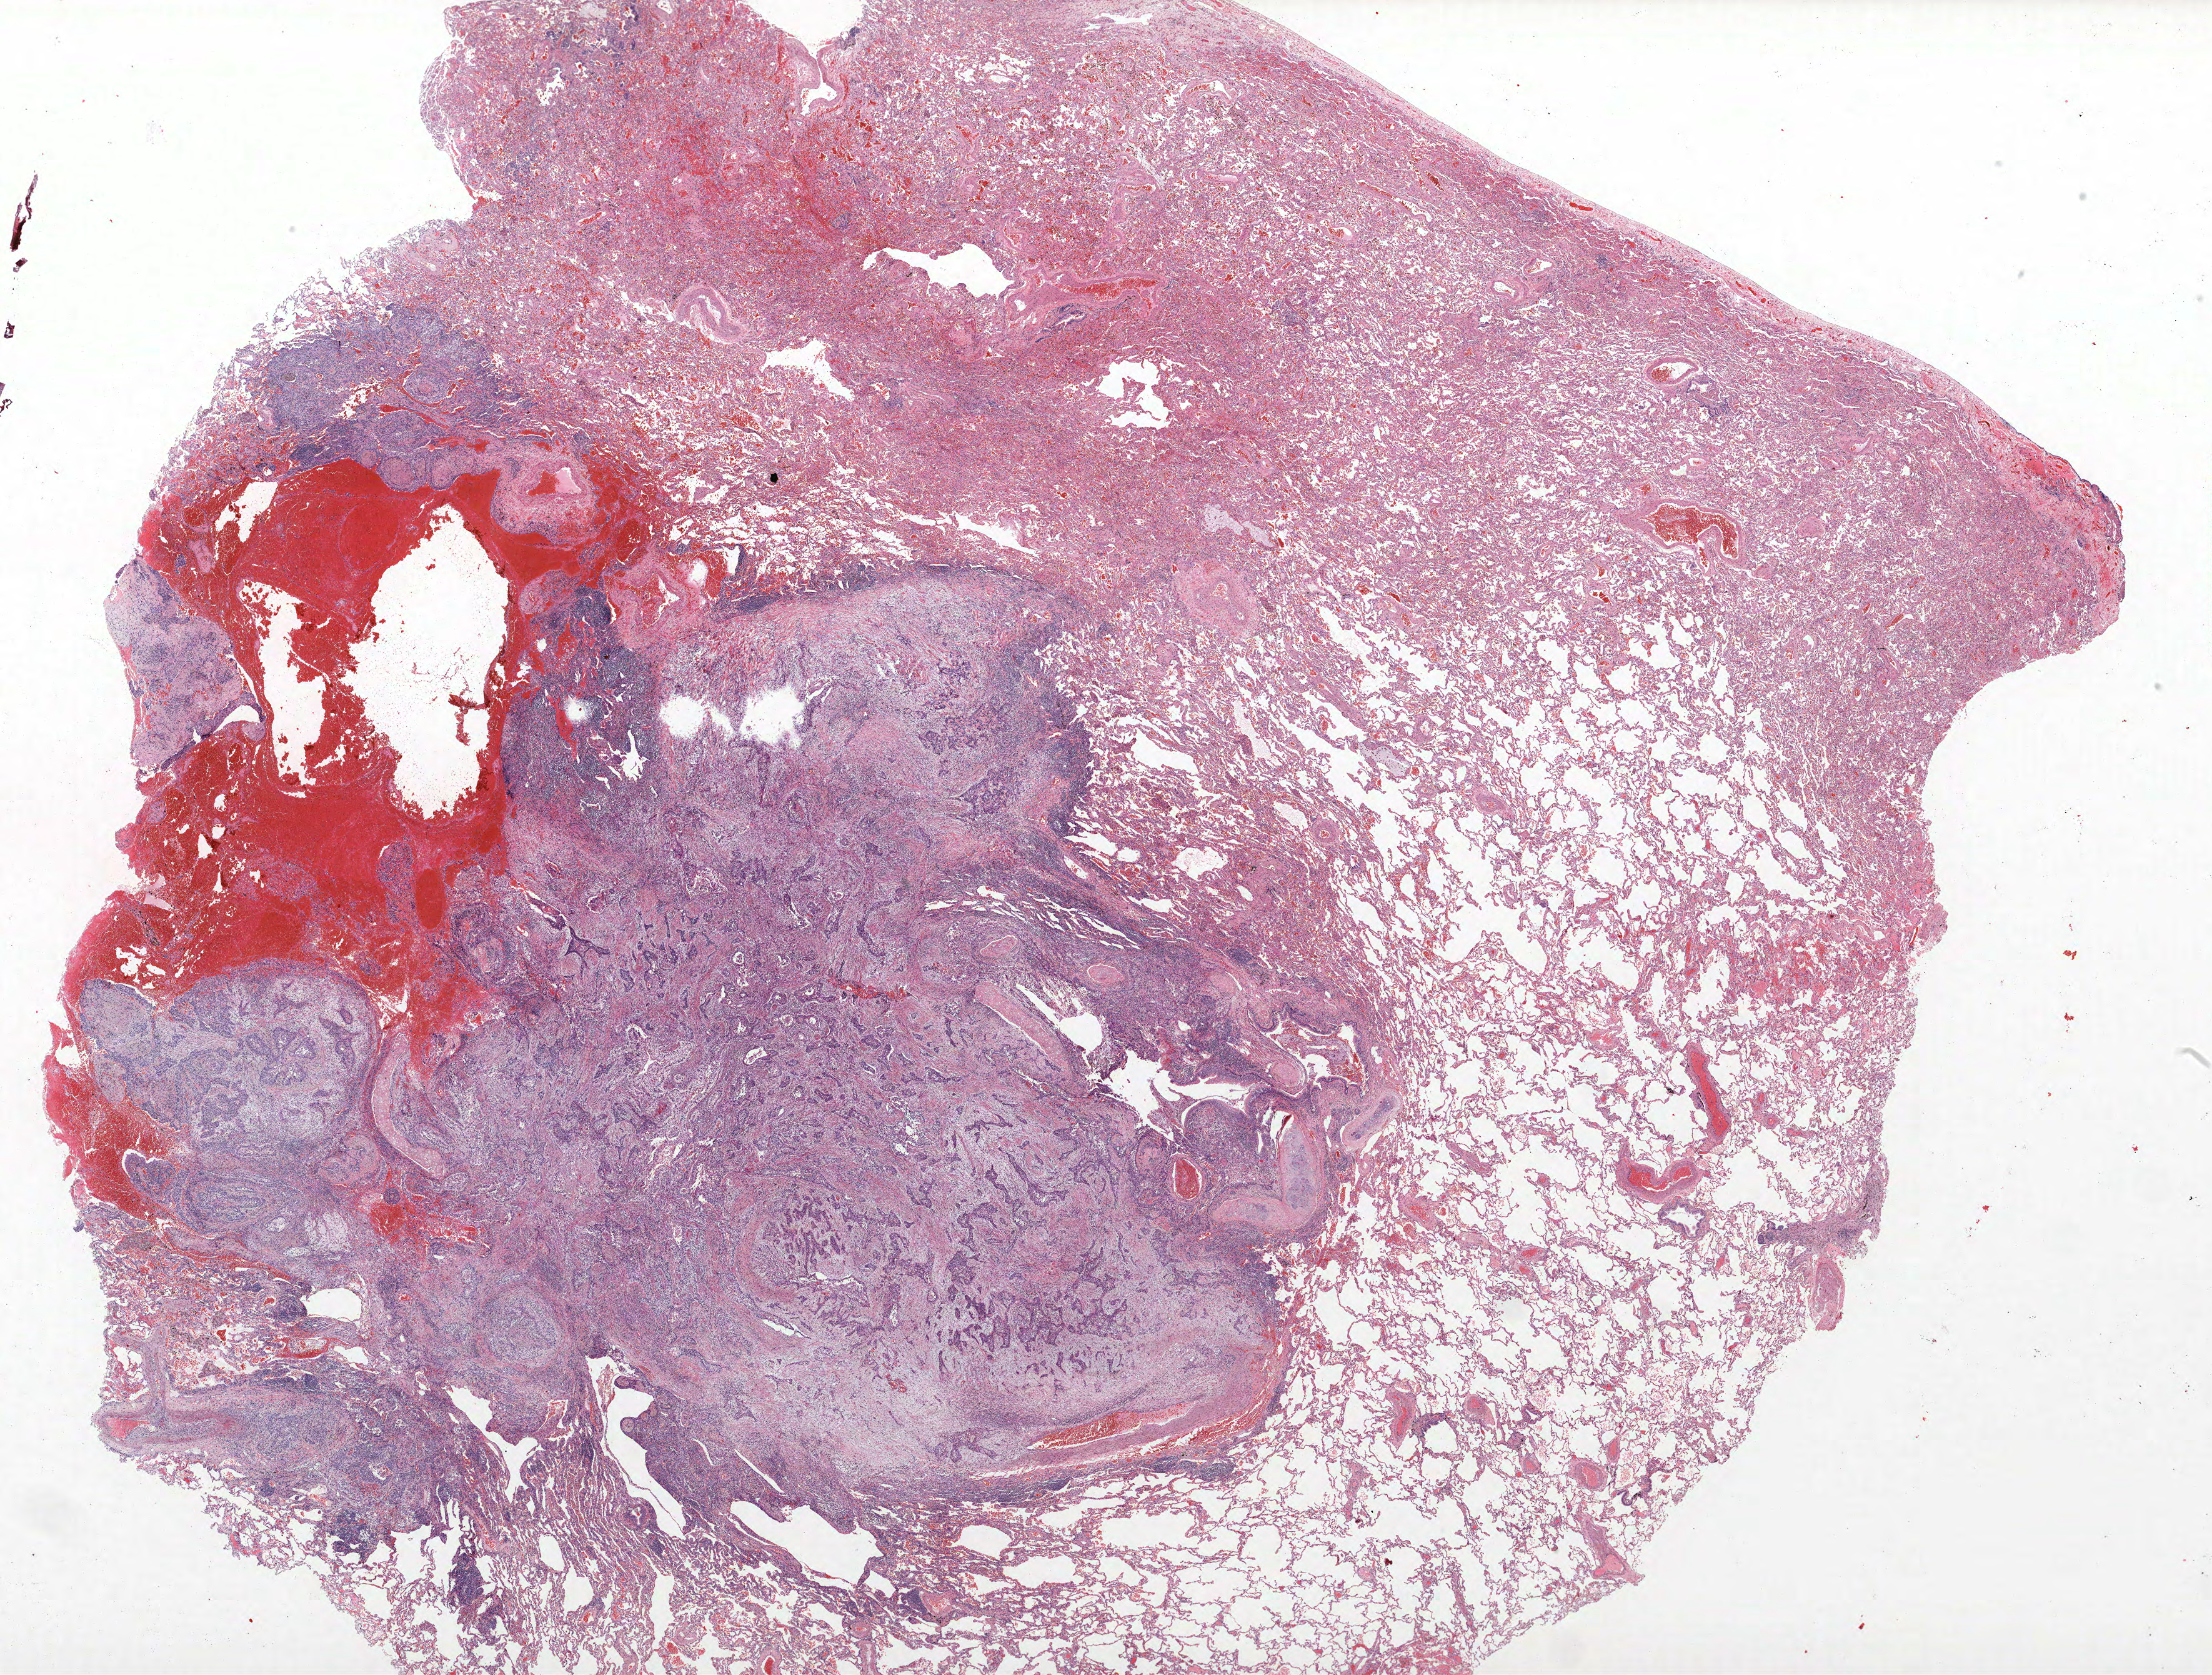
Whole-slide histology image, H&E, whole scanned area (about 28.3 x 21.4 mm, acquisition: 40x scan) shown as a low-resolution overview. Formalin-fixed paraffin-embedded (FFPE) section. Lung. Male patient, aged 57 at enrolment. Current smoker at enrolment. Grade: moderately differentiated (G2).
• stage (AJCC 6th edition): IA
• ICD-O-3 topography: lower lobe of lung (C34.3)
• tumour size (pathology): 22 mm
• participant's lung-cancer diagnosis: Squamous cell carcinoma, NOS (ICD-O-3 8070/3)
• primary tumour location (clinical record): left lower lobe